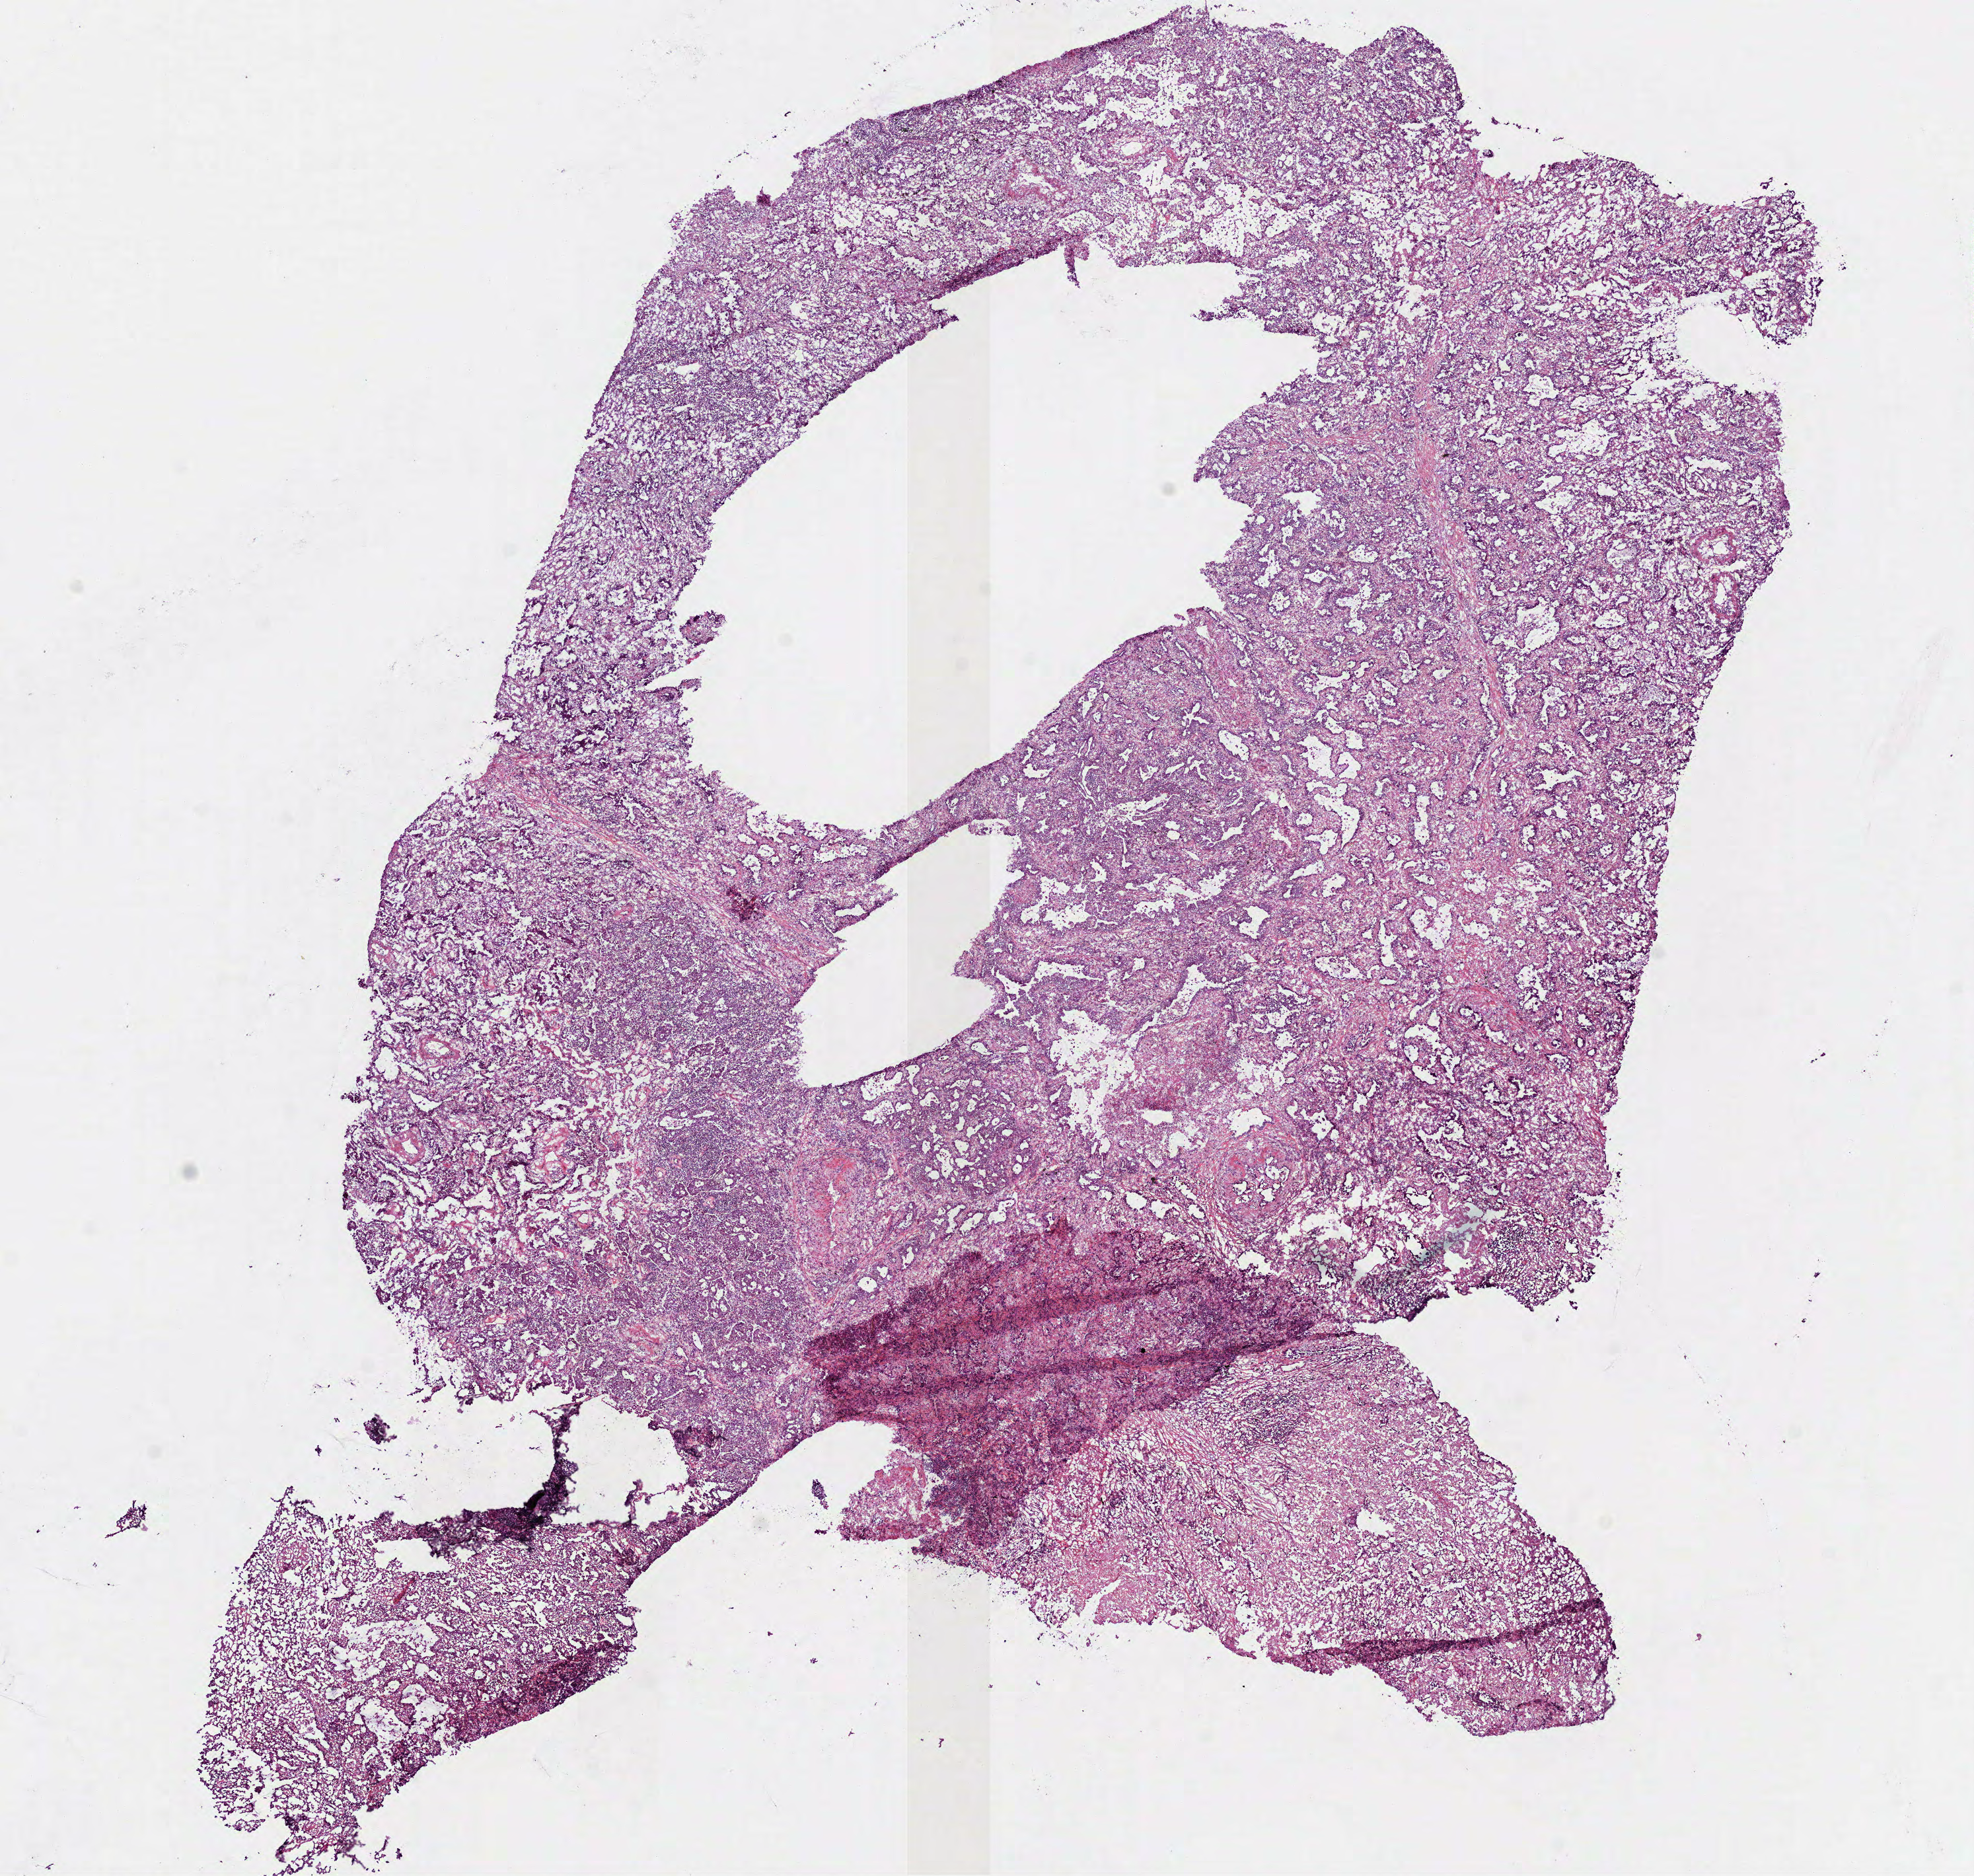
Digitized Hematoxylin and eosin (H&E) stained tissue section (whole slide), a low-resolution overview of the entire scanned area, about 12.0 x 11.4 mm; frozen section from the bottom of the tissue portion; lung, primary tumour sample. Female patient; age at initial diagnosis 70 years. Composition of this section per pathologist review: tumour cells 80%, tumour nuclei 65%, normal cells 0%, stromal cells 20%, necrosis 0%.
AJCC pathologic stage: IIIA. Laterality: left. Histologic diagnosis: Adenocarcinoma, NOS (upper lobe, lung).